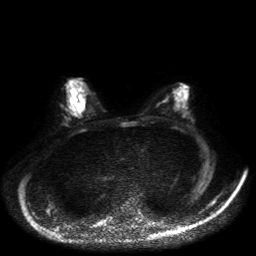
Breast MRI, one axial slice; slice 23 of 50 in the series (ordered by position); diffusion-weighted series; image 2 of 4 stored at this slice position (different b-values; order by instance number); 1.5 T; 4 mm slice thickness; 256 × 256 image matrix, field of view 360 × 360 mm. Female patient.
Structures marked on this image (outlined manually by an expert reader):
- tumour on diffusion-weighted imaging: bounding box [x1, y1, x2, y2] px = [77, 103, 82, 107]